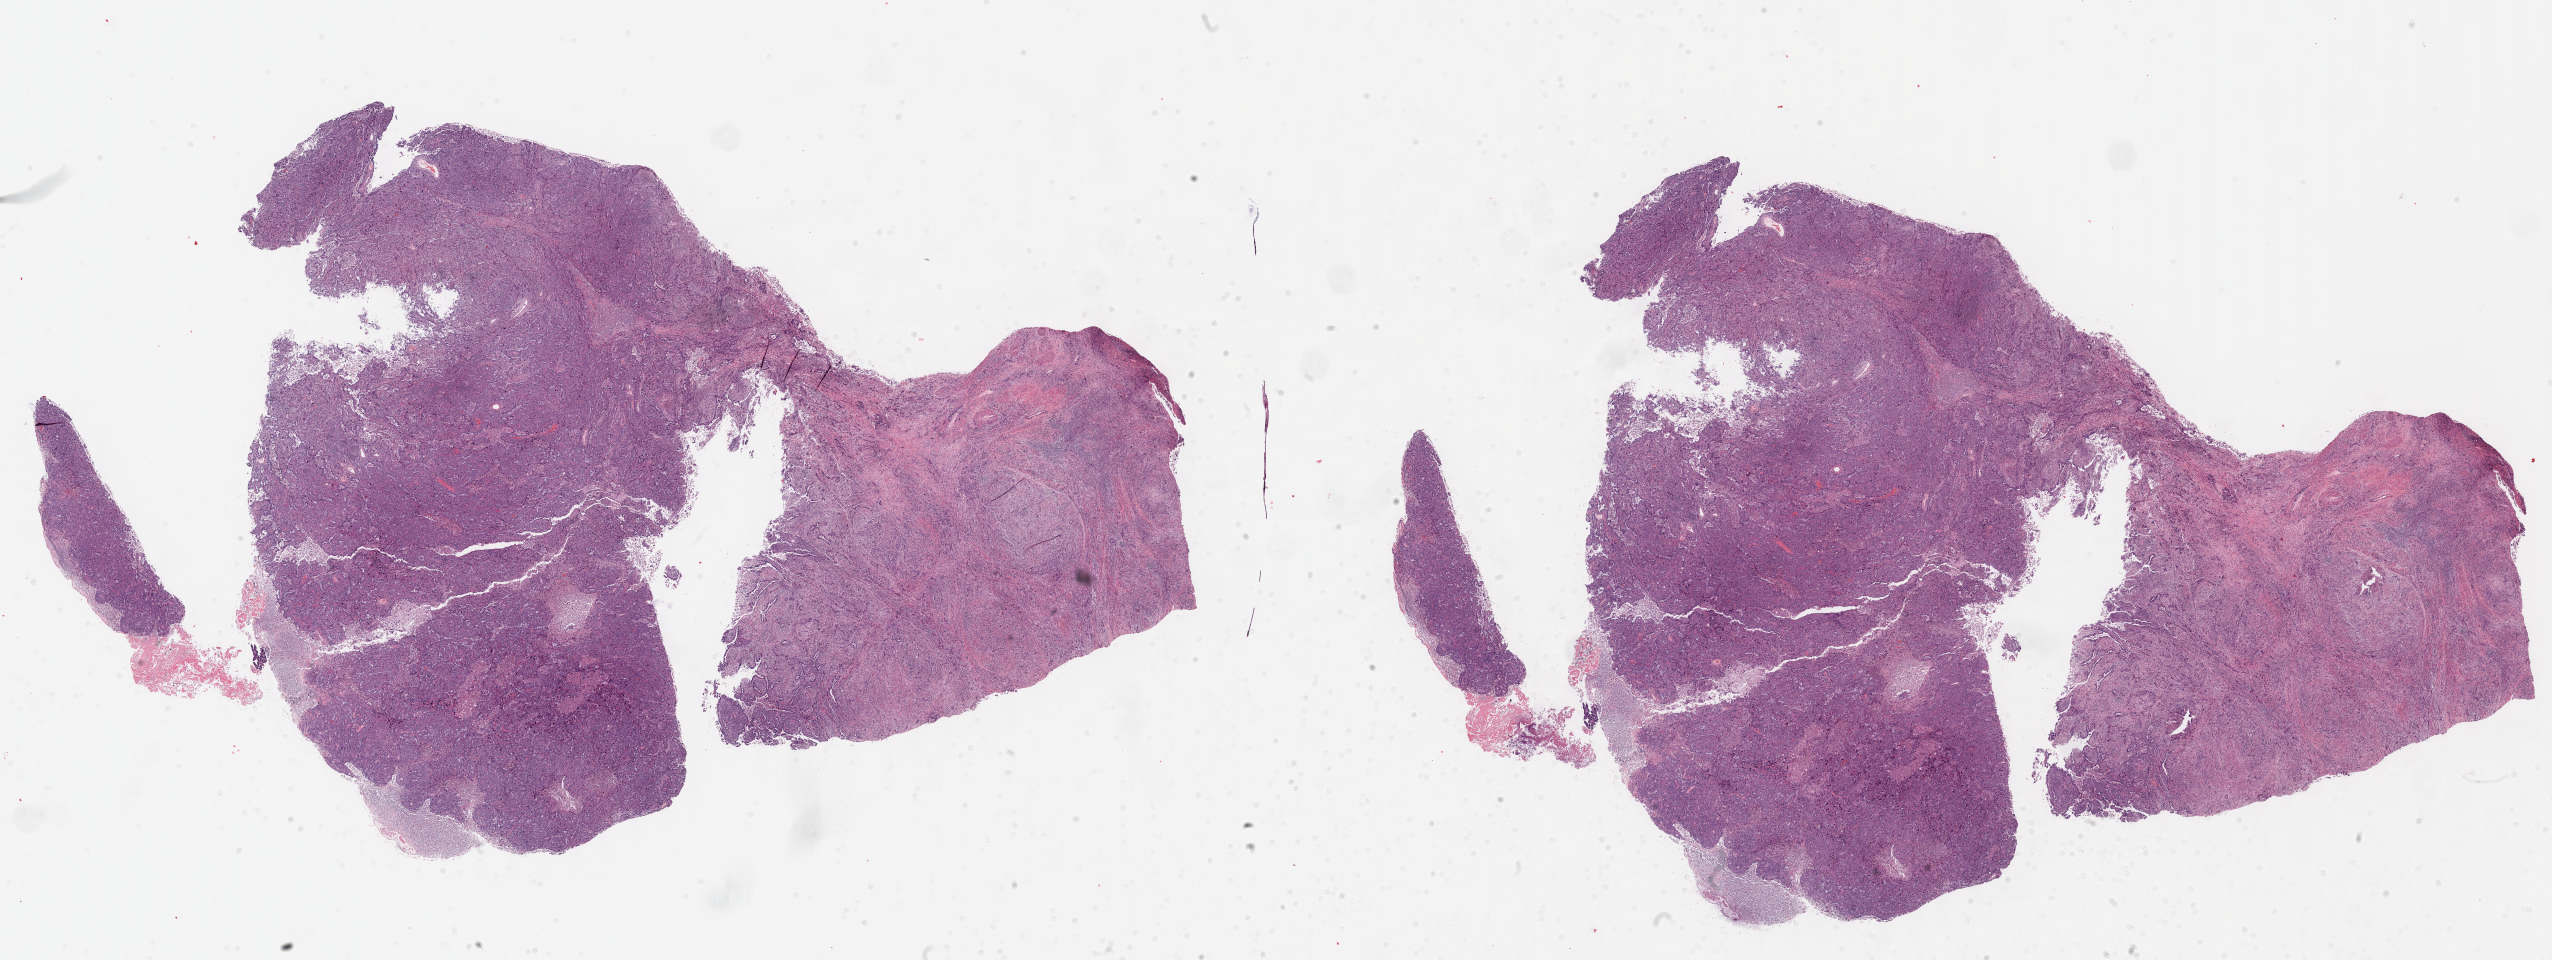
Digitized Hematoxylin and eosin (H&E) stained tissue section (whole slide), whole scanned area (about 41.2 x 15.5 mm) shown as a low-resolution overview; formalin-fixed paraffin-embedded (FFPE) diagnostic section; sample: primary tumour, uterus. Female, age 56 years at initial diagnosis. Histologic grade: G3 (poorly differentiated).
FIGO stage: IIIC1. Pathologic diagnosis: Serous cystadenocarcinoma, NOS (endometrium).